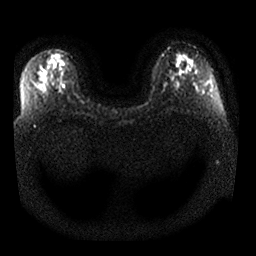
Breast MRI, one axial slice. Position 16 of 25 along the scan axis. Diffusion-weighted series; image 2 of 4 stored at this slice position (different b-values; order by instance number). 1.5 T. 4 mm slice thickness. 256 × 256 image matrix. Female patient.
Annotated regions visible in this slice (outlined manually by an expert reader):
- tumour on diffusion-weighted imaging: bounding box (x1, y1, x2, y2) in pixels: (47, 52, 65, 65)